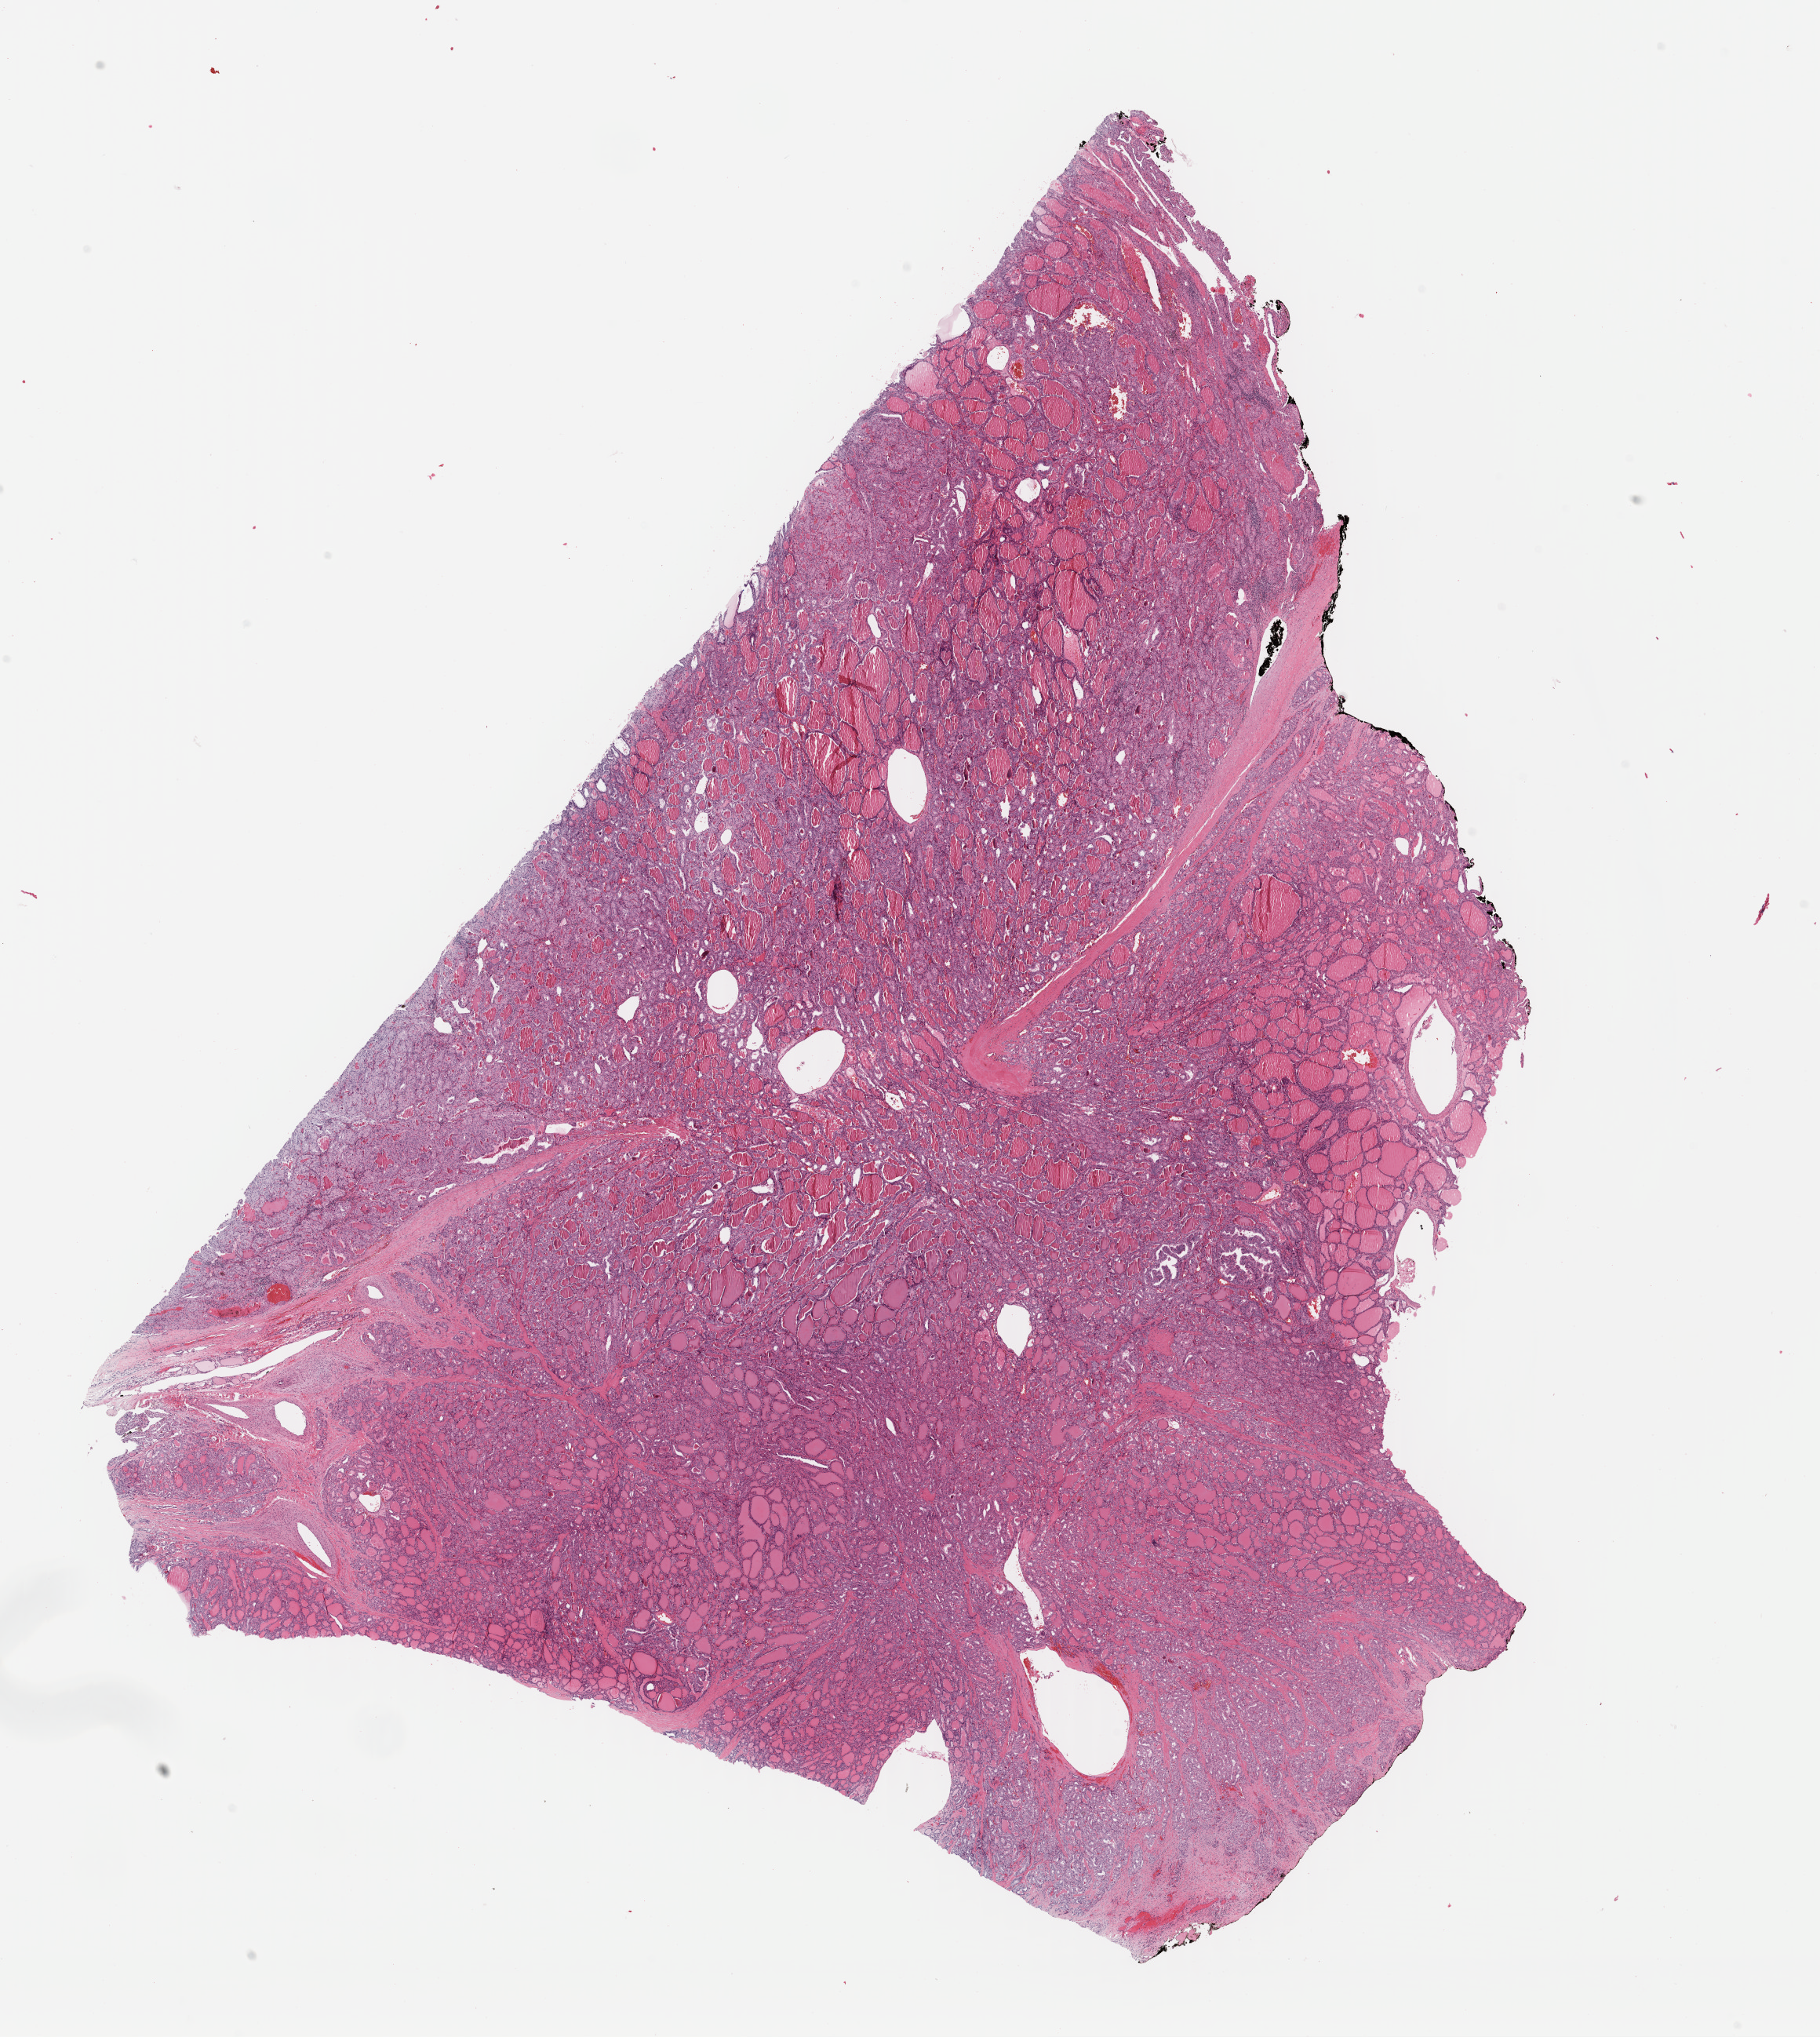
Hematoxylin and eosin (H&E) stained whole-slide image — shown as a low-resolution overview of the whole scanned area (about 18.2 x 20.4 mm), formalin-fixed paraffin-embedded (FFPE) diagnostic section, thyroid, primary tumour sample. Female patient; age at initial diagnosis 36 years.
Lymph nodes positive (case pathology): 0 of 1 examined. AJCC pathologic stage: I. Histologic diagnosis: Papillary adenocarcinoma, NOS (thyroid gland). Laterality: bilateral.